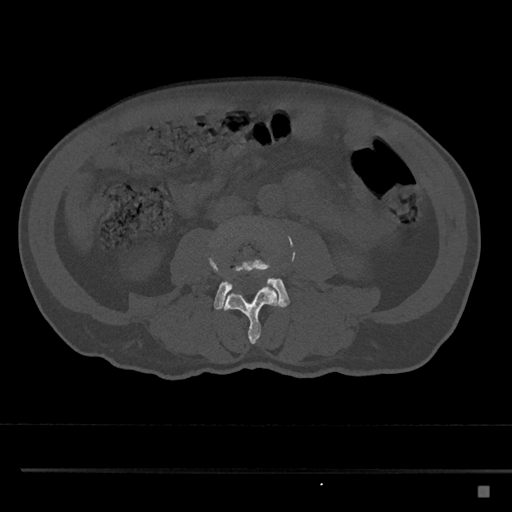
CT including the spine, one axial slice; reconstruction kernel Br40s/3; 120 kVp; bone window (W 1800 / L 400 HU); 0.5 mm slice thickness; 512 × 512 image matrix, field of view 391 × 391 mm. Male patient, age 59 years. From the clinical record (not read from this slice): primary cancer: prostate.
Outlined on this slice (semi-automatic segmentation, software-assisted and operator-edited):
- L3 vertebra: bounding box [x1, y1, x2, y2] px = [209, 224, 280, 344]
- L4 vertebra: [213, 257, 290, 310]